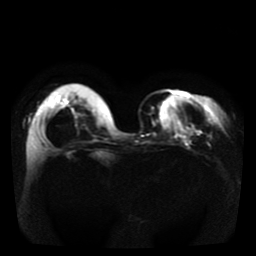
Breast MRI, one axial slice; slice 12 of 41 in the series (ordered by position); diffusion-weighted series; image 2 of 4 stored at this slice position (different b-values; order by instance number); 1.5 T; 5 mm slice thickness; 256 × 256 image matrix. Female patient.
Annotated regions visible in this slice (manually delineated by an expert):
- tumour on diffusion-weighted imaging: bounding box [x1, y1, x2, y2] px = [193, 128, 196, 131]